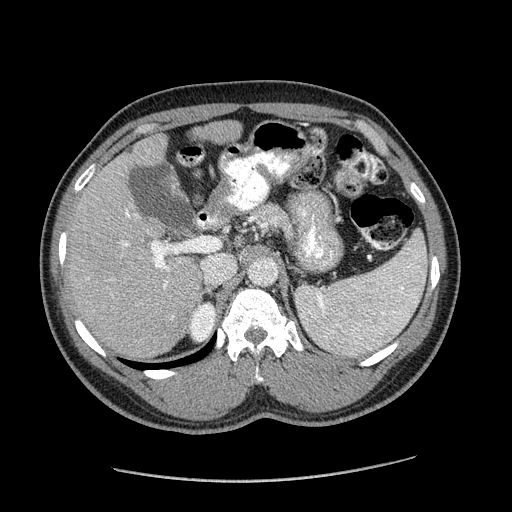
Contrast-enhanced abdominal CT (liver protocol), one axial slice. Position 113 of 182 along the scan axis. Reconstruction kernel STANDARD. Soft-tissue window (W 400 / L 40 HU). 512 × 512 image matrix, field of view 400 × 400 mm. Case-level facts recorded for this patient, not image findings: diagnosis: hepatocellular carcinoma (patient treated with transarterial chemoembolisation; whether this scan precedes or follows treatment is not stated here); TNM stage (as recorded): Stage-I; Child-Pugh class: A; tumour differentiation: well differentiated; tumour nodularity: uninodular.
Annotated regions visible in this slice (semi-automatic segmentation, software-assisted and operator-edited):
- liver parenchyma outside the tumour (the mass and vessels are separate outlines, so this box may not span the whole liver): bounding box [x1, y1, x2, y2] px = [66, 120, 242, 358]
- liver vessels: [88, 210, 177, 318]